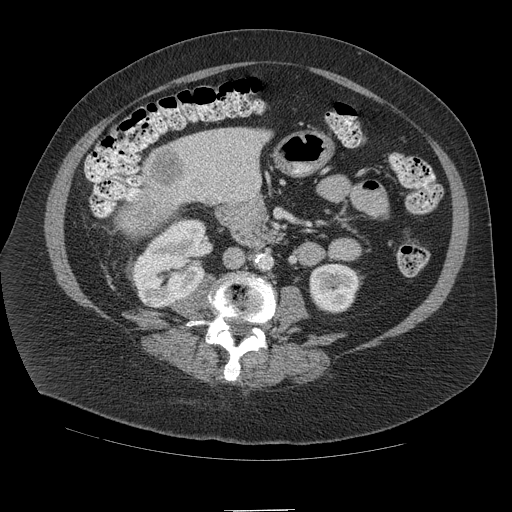
Contrast-enhanced abdominal CT (liver protocol), one axial slice. Position 30 of 109 along the scan axis. Reconstruction kernel STANDARD. 140 kVp. Soft-tissue window (W 400 / L 40 HU). 512 × 512 image matrix, field of view 420 × 420 mm. Case-level facts recorded for this patient, not image findings: diagnosis: hepatocellular carcinoma (patient treated with transarterial chemoembolisation; whether this scan precedes or follows treatment is not stated here); TNM stage (as recorded): Stage-IVB; Child-Pugh class: A; tumour differentiation: poorly differentiated; tumour nodularity: multinodular.
Outlined on this slice (semi-automatically segmented with operator editing):
- liver parenchyma outside the tumour (the mass and vessels are separate outlines, so this box may not span the whole liver): box from (x=149, y=126) to (x=270, y=206) px
- mass: (x=117, y=143)–(x=193, y=237)
- liver vessels: (x=183, y=164)–(x=241, y=199)